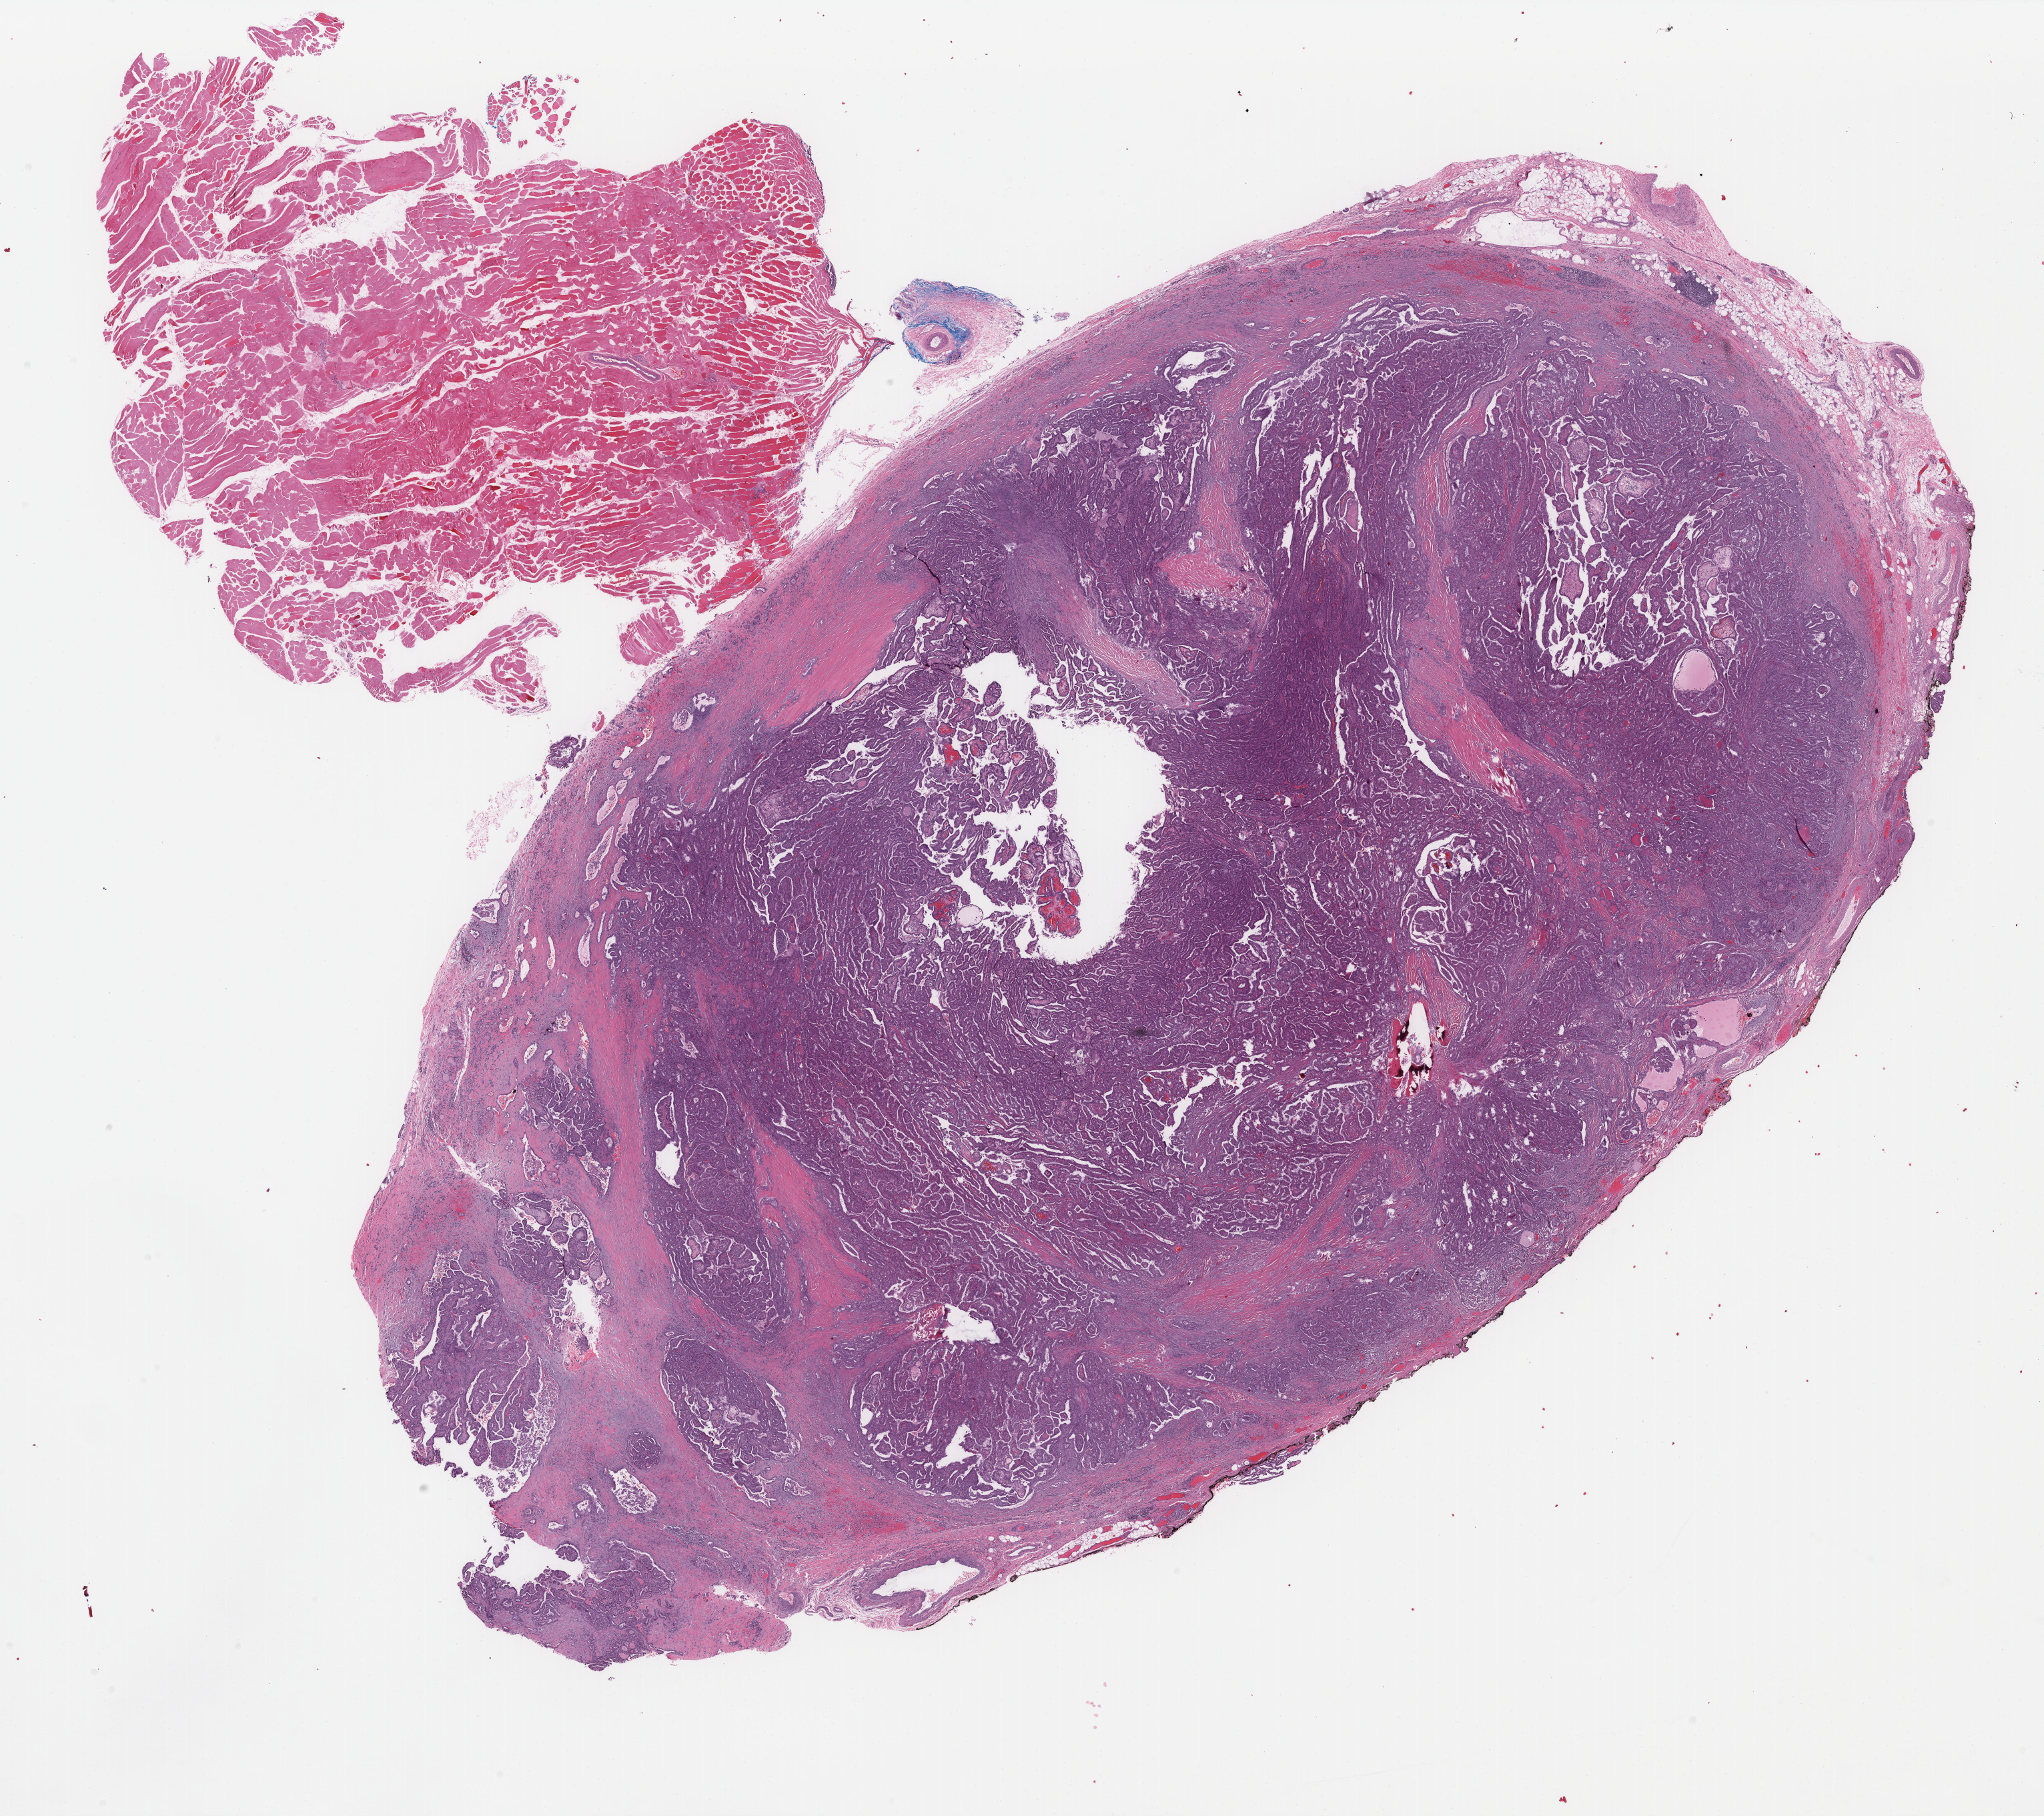
H&E-stained whole-slide image, shown as a low-resolution overview of the whole scanned area (about 24.3 x 21.6 mm). Formalin-fixed paraffin-embedded (FFPE) diagnostic section. Thyroid, primary tumour sample. Female, age 46 years at initial diagnosis.
* pathologic diagnosis: Papillary carcinoma, columnar cell (thyroid gland)
* laterality: bilateral
* AJCC pathologic stage: III (7th edition)
* lymph nodes positive (case pathology): 1 of 2 examined